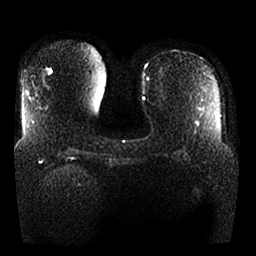
Breast MRI, one axial slice. Position 7 of 25 along the scan axis. Diffusion-weighted series; image 2 of 4 stored at this slice position (different b-values; order by instance number). 1.5 T. 256 × 256 image matrix, field of view 360 × 360 mm. Female patient.
Annotated regions visible in this slice (expert manual segmentation):
- tumour on diffusion-weighted imaging: bounding box <48,69,51,73> (left, top, right, bottom; pixels)